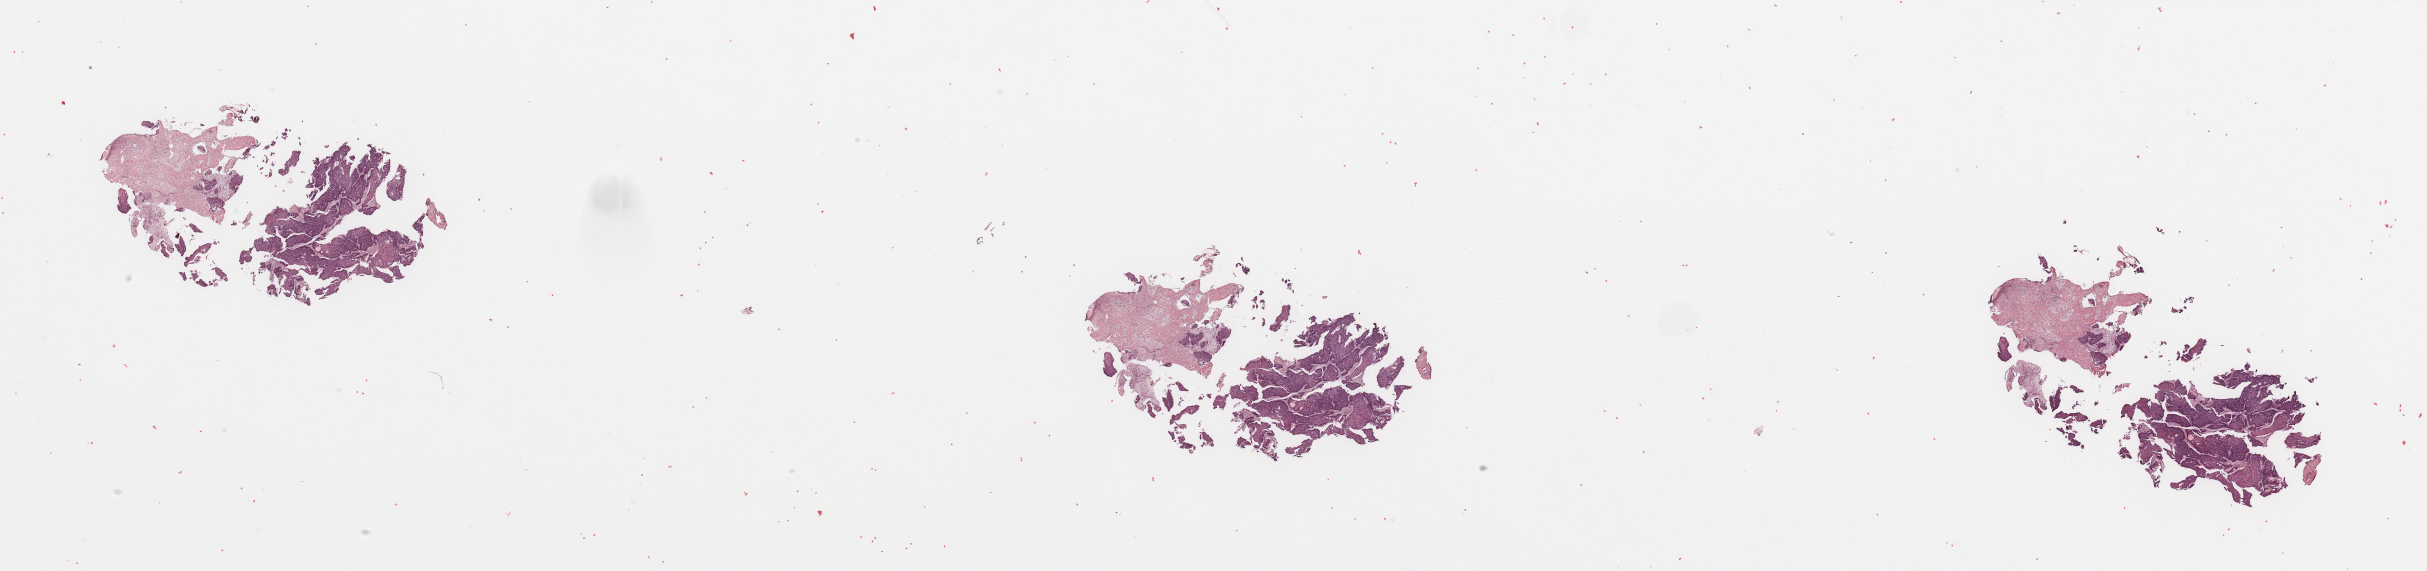
Digitized H&E-stained tissue section (whole slide), a low-resolution overview of the entire scanned area, about 38.4 x 9.0 mm (acquisition: 20x scan). Tumour tissue sample, sampled site: tongue. Male, 66 y/o. Histologic grade: G2 (moderately differentiated). Pathologist review of this section (percent, as recorded): tumour nuclei 80%, necrosis 10%.
- diagnosis: Squamous cell carcinoma, NOS
- AJCC pathologic stage: I
- primary tumour site (as recorded): oral cavity